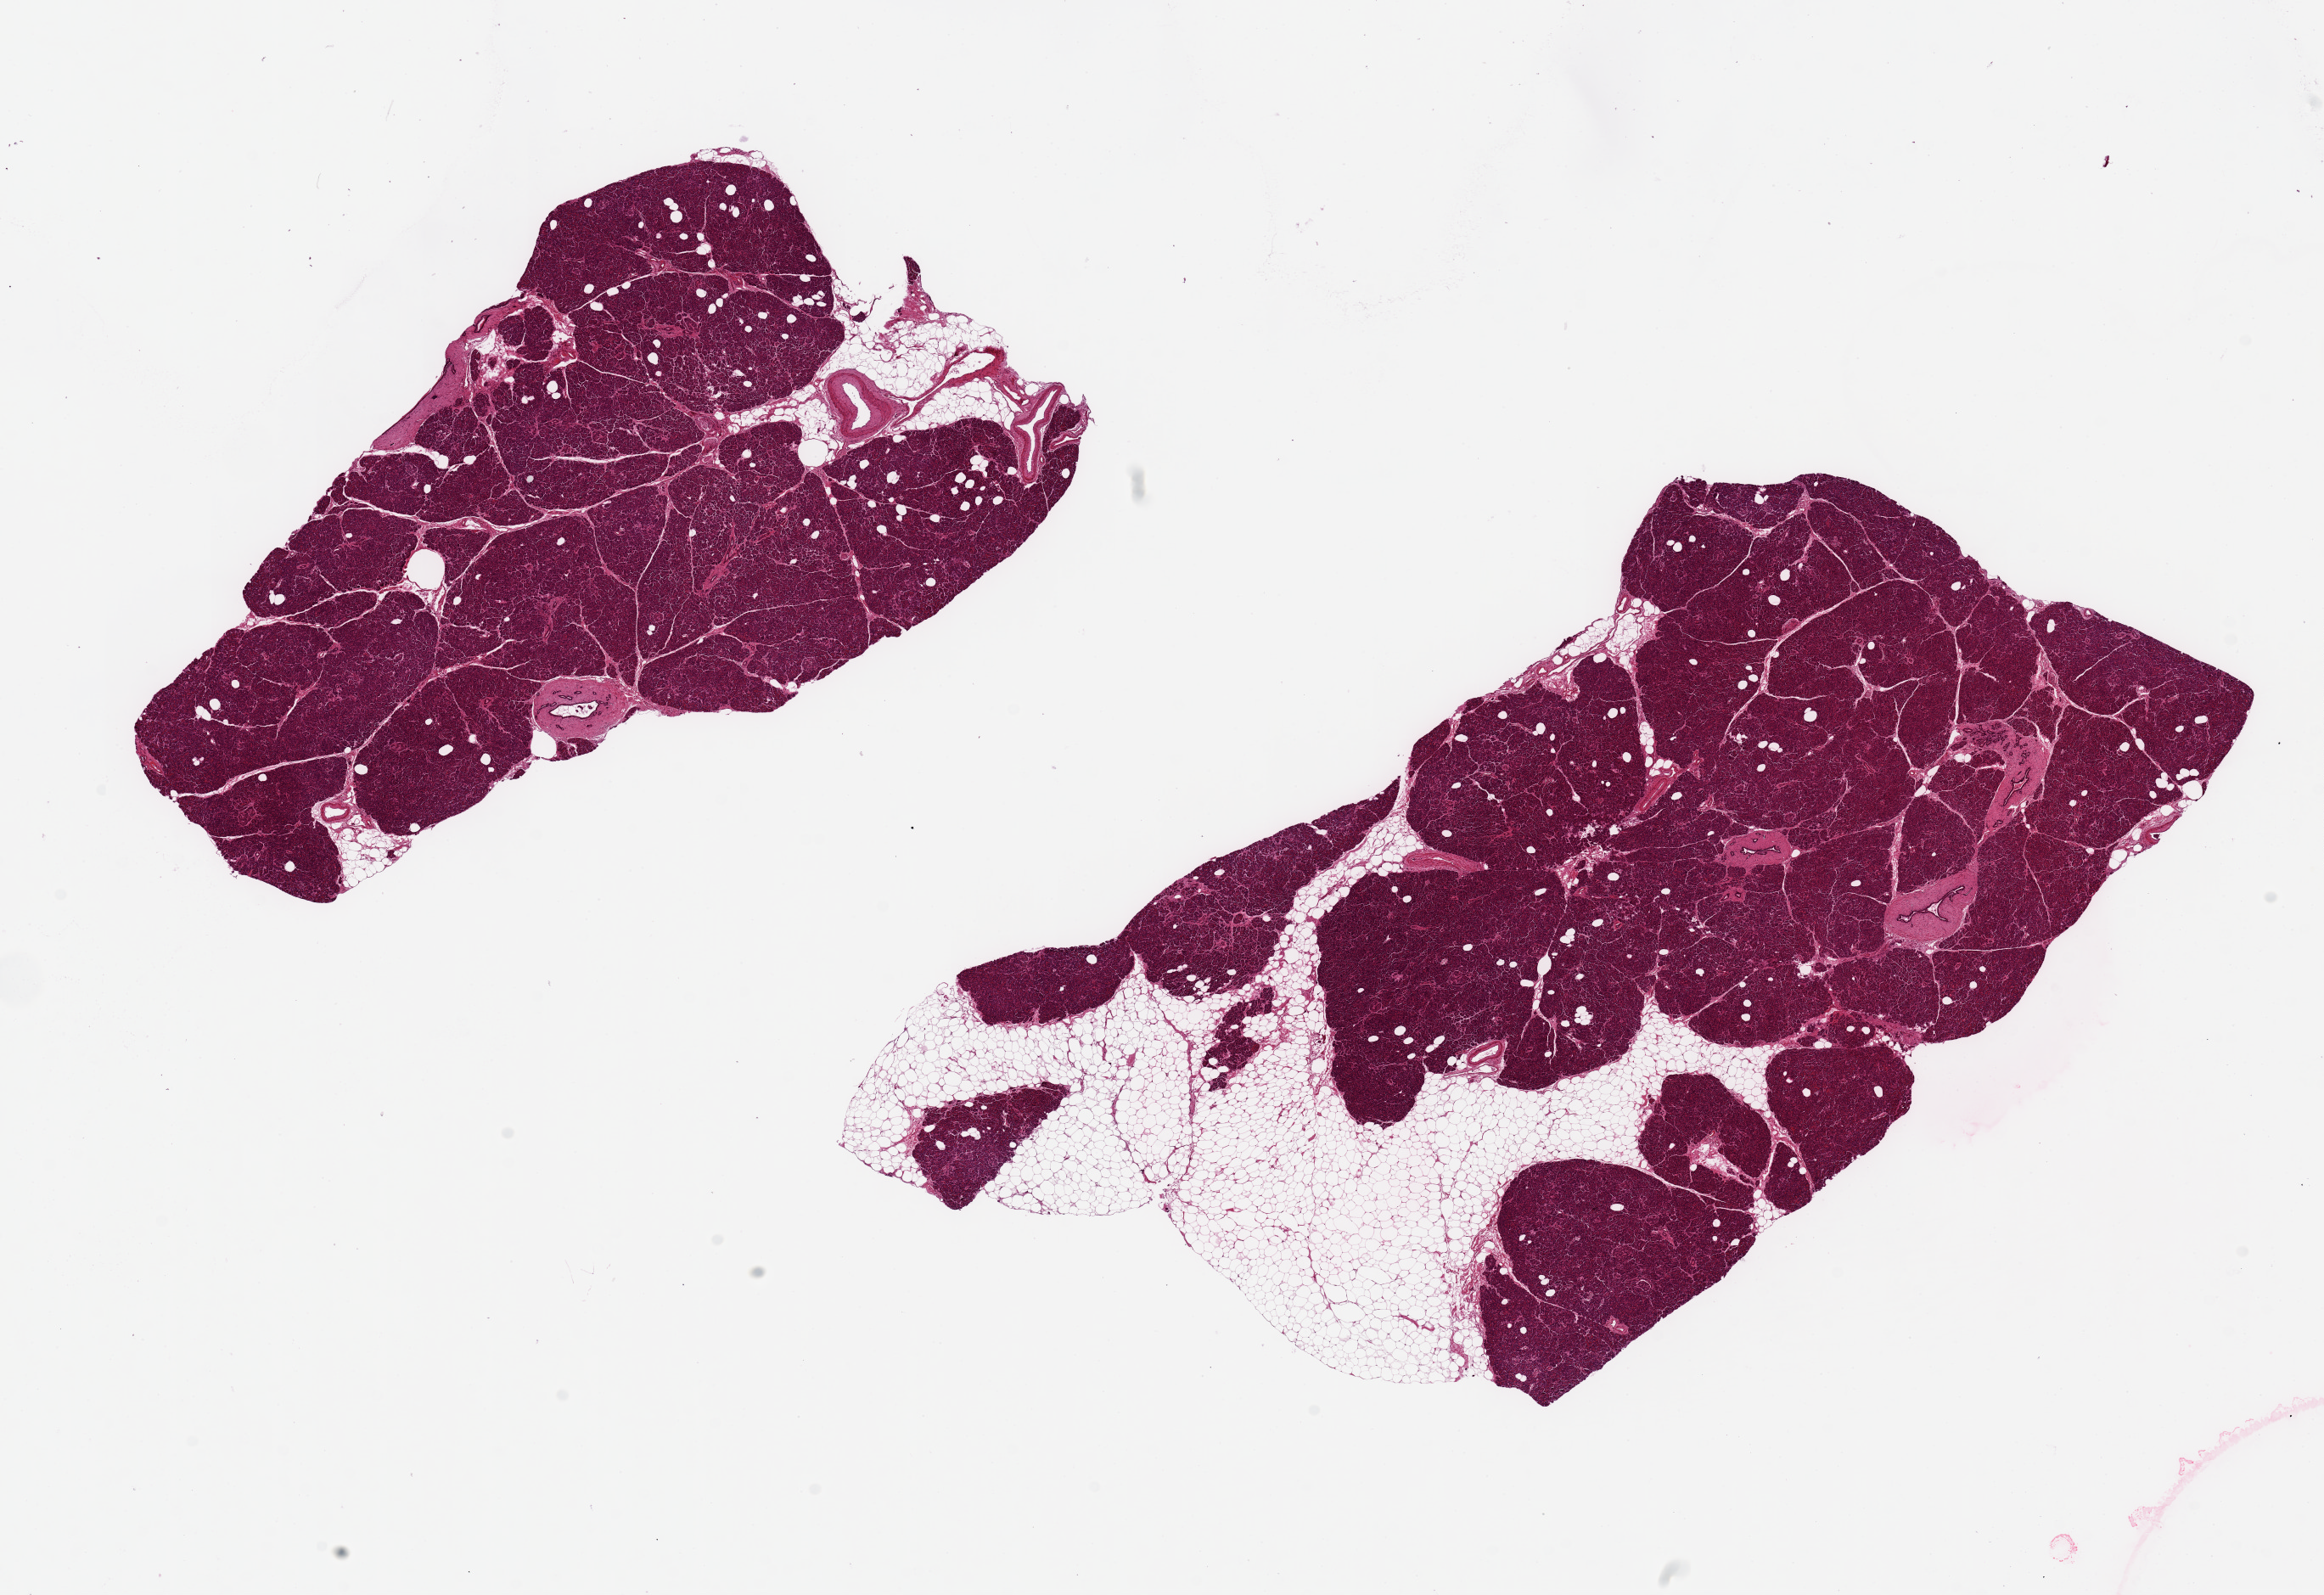
Whole-slide image, hematoxylin and eosin (H&E) stain, shown as a low-resolution overview of the whole scanned area (about 21.7 x 14.9 mm, slide scanned at 20x). PAXgene-fixed, paraffin-embedded tissue. Section of pancreas (target tissue). Tissue donor sample.
Review note (as recorded): 2 pieces ~9x5mm; Well preserved; one aliquot is ~20 fat on one pole; Branching non dysplastic ductal elements noted in both; Fatty areas; Islets well seen.